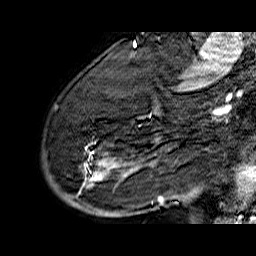
Breast MRI (dynamic contrast-enhanced), one sagittal slice. Slice 46 of 60 in the series (ordered by position). Dynamic contrast-enhanced series, time point 2 of 6 at this slice position (early post-contrast). 1.5 T. TE 6.5 ms, TR 32.9 ms. 256 × 256 image matrix. Female patient. From the clinical record (not read from this slice): setting: breast cancer imaged before/during neoadjuvant chemotherapy; receptor status: HR-positive, HER2-negative.
Structures marked on this image (semi-automatically segmented with operator editing):
- analysis volume of interest (the breast-tissue region the enhancement analysis was run in; not a lesion): box from (x=43, y=74) to (x=176, y=210) px
- tumour enhancement mask (voxels above the 100 % enhancement threshold inside the analysis volume of interest): (x=85, y=111)–(x=163, y=202)